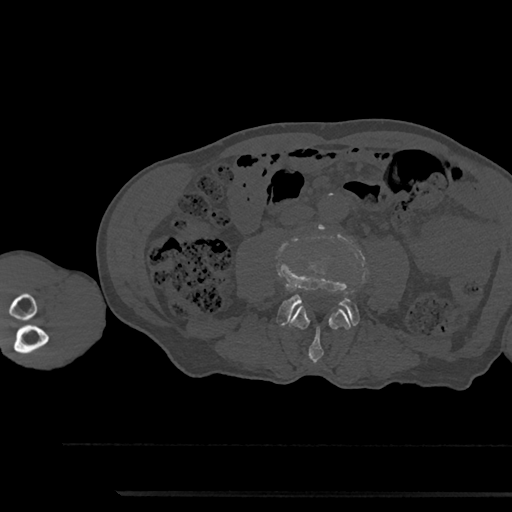
CT including the spine, one axial slice; slice 447 of 797 in the series (ordered by position); reconstruction kernel Br40s/3; bone window (W 1800 / L 400 HU); 512 × 512 image matrix, field of view 367 × 367 mm. Male patient, age 79 years. From the clinical record (not read from this slice): primary cancer: prostate.
Annotated regions visible in this slice (semi-automatically segmented with operator editing):
- L3 vertebra: bounding box (x1, y1, x2, y2) in pixels: (289, 305, 351, 363)
- L4 vertebra: (278, 259, 359, 326)